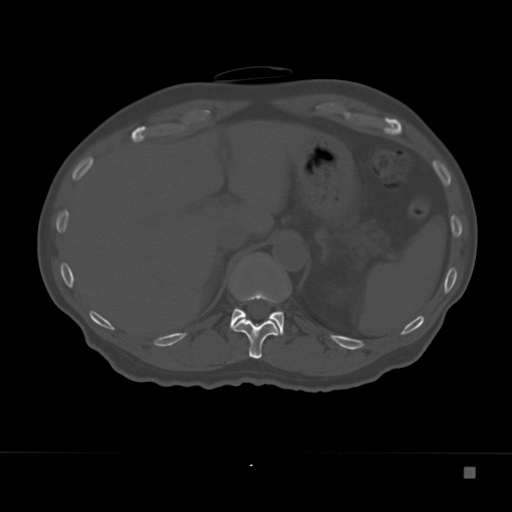
CT including the spine, one axial slice; slice 144 of 332 in the series (ordered by position); reconstruction kernel Br40s; bone window (W 1800 / L 400 HU); 1.5 mm slice thickness; 512 × 512 image matrix. Male patient, age 72 years. Case-level facts recorded for this patient, not image findings: primary cancer: skeletal.
Annotated regions visible in this slice (semi-automatically segmented with operator editing):
- T11 vertebra: box from (x=230, y=290) to (x=288, y=359) px
- T12 vertebra: (x=230, y=262)–(x=284, y=335)